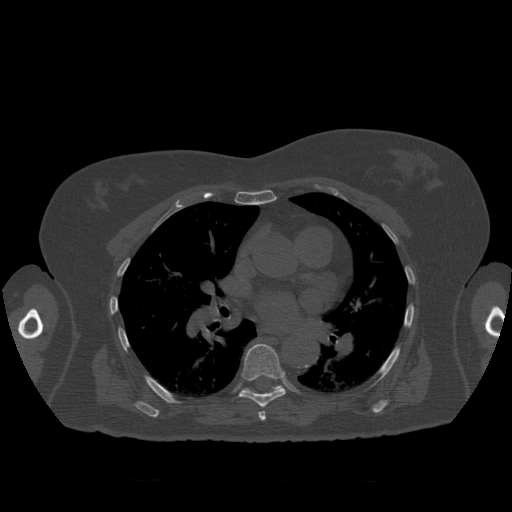
CT including the spine, one axial slice. Position 394 of 399 along the scan axis. Reconstruction kernel STANDARD. Bone window (W 1800 / L 400 HU). 1.25 mm slice thickness. 512 × 512 image matrix, field of view 404 × 404 mm. Patient age 81 years. Case-level facts recorded for this patient, not image findings: primary cancer: renal.
Outlined on this slice (semi-automatic segmentation, software-assisted and operator-edited):
- T7 vertebra: bounding box <238,344,286,421> (left, top, right, bottom; pixels)
- T8 vertebra: <243,385,284,394>